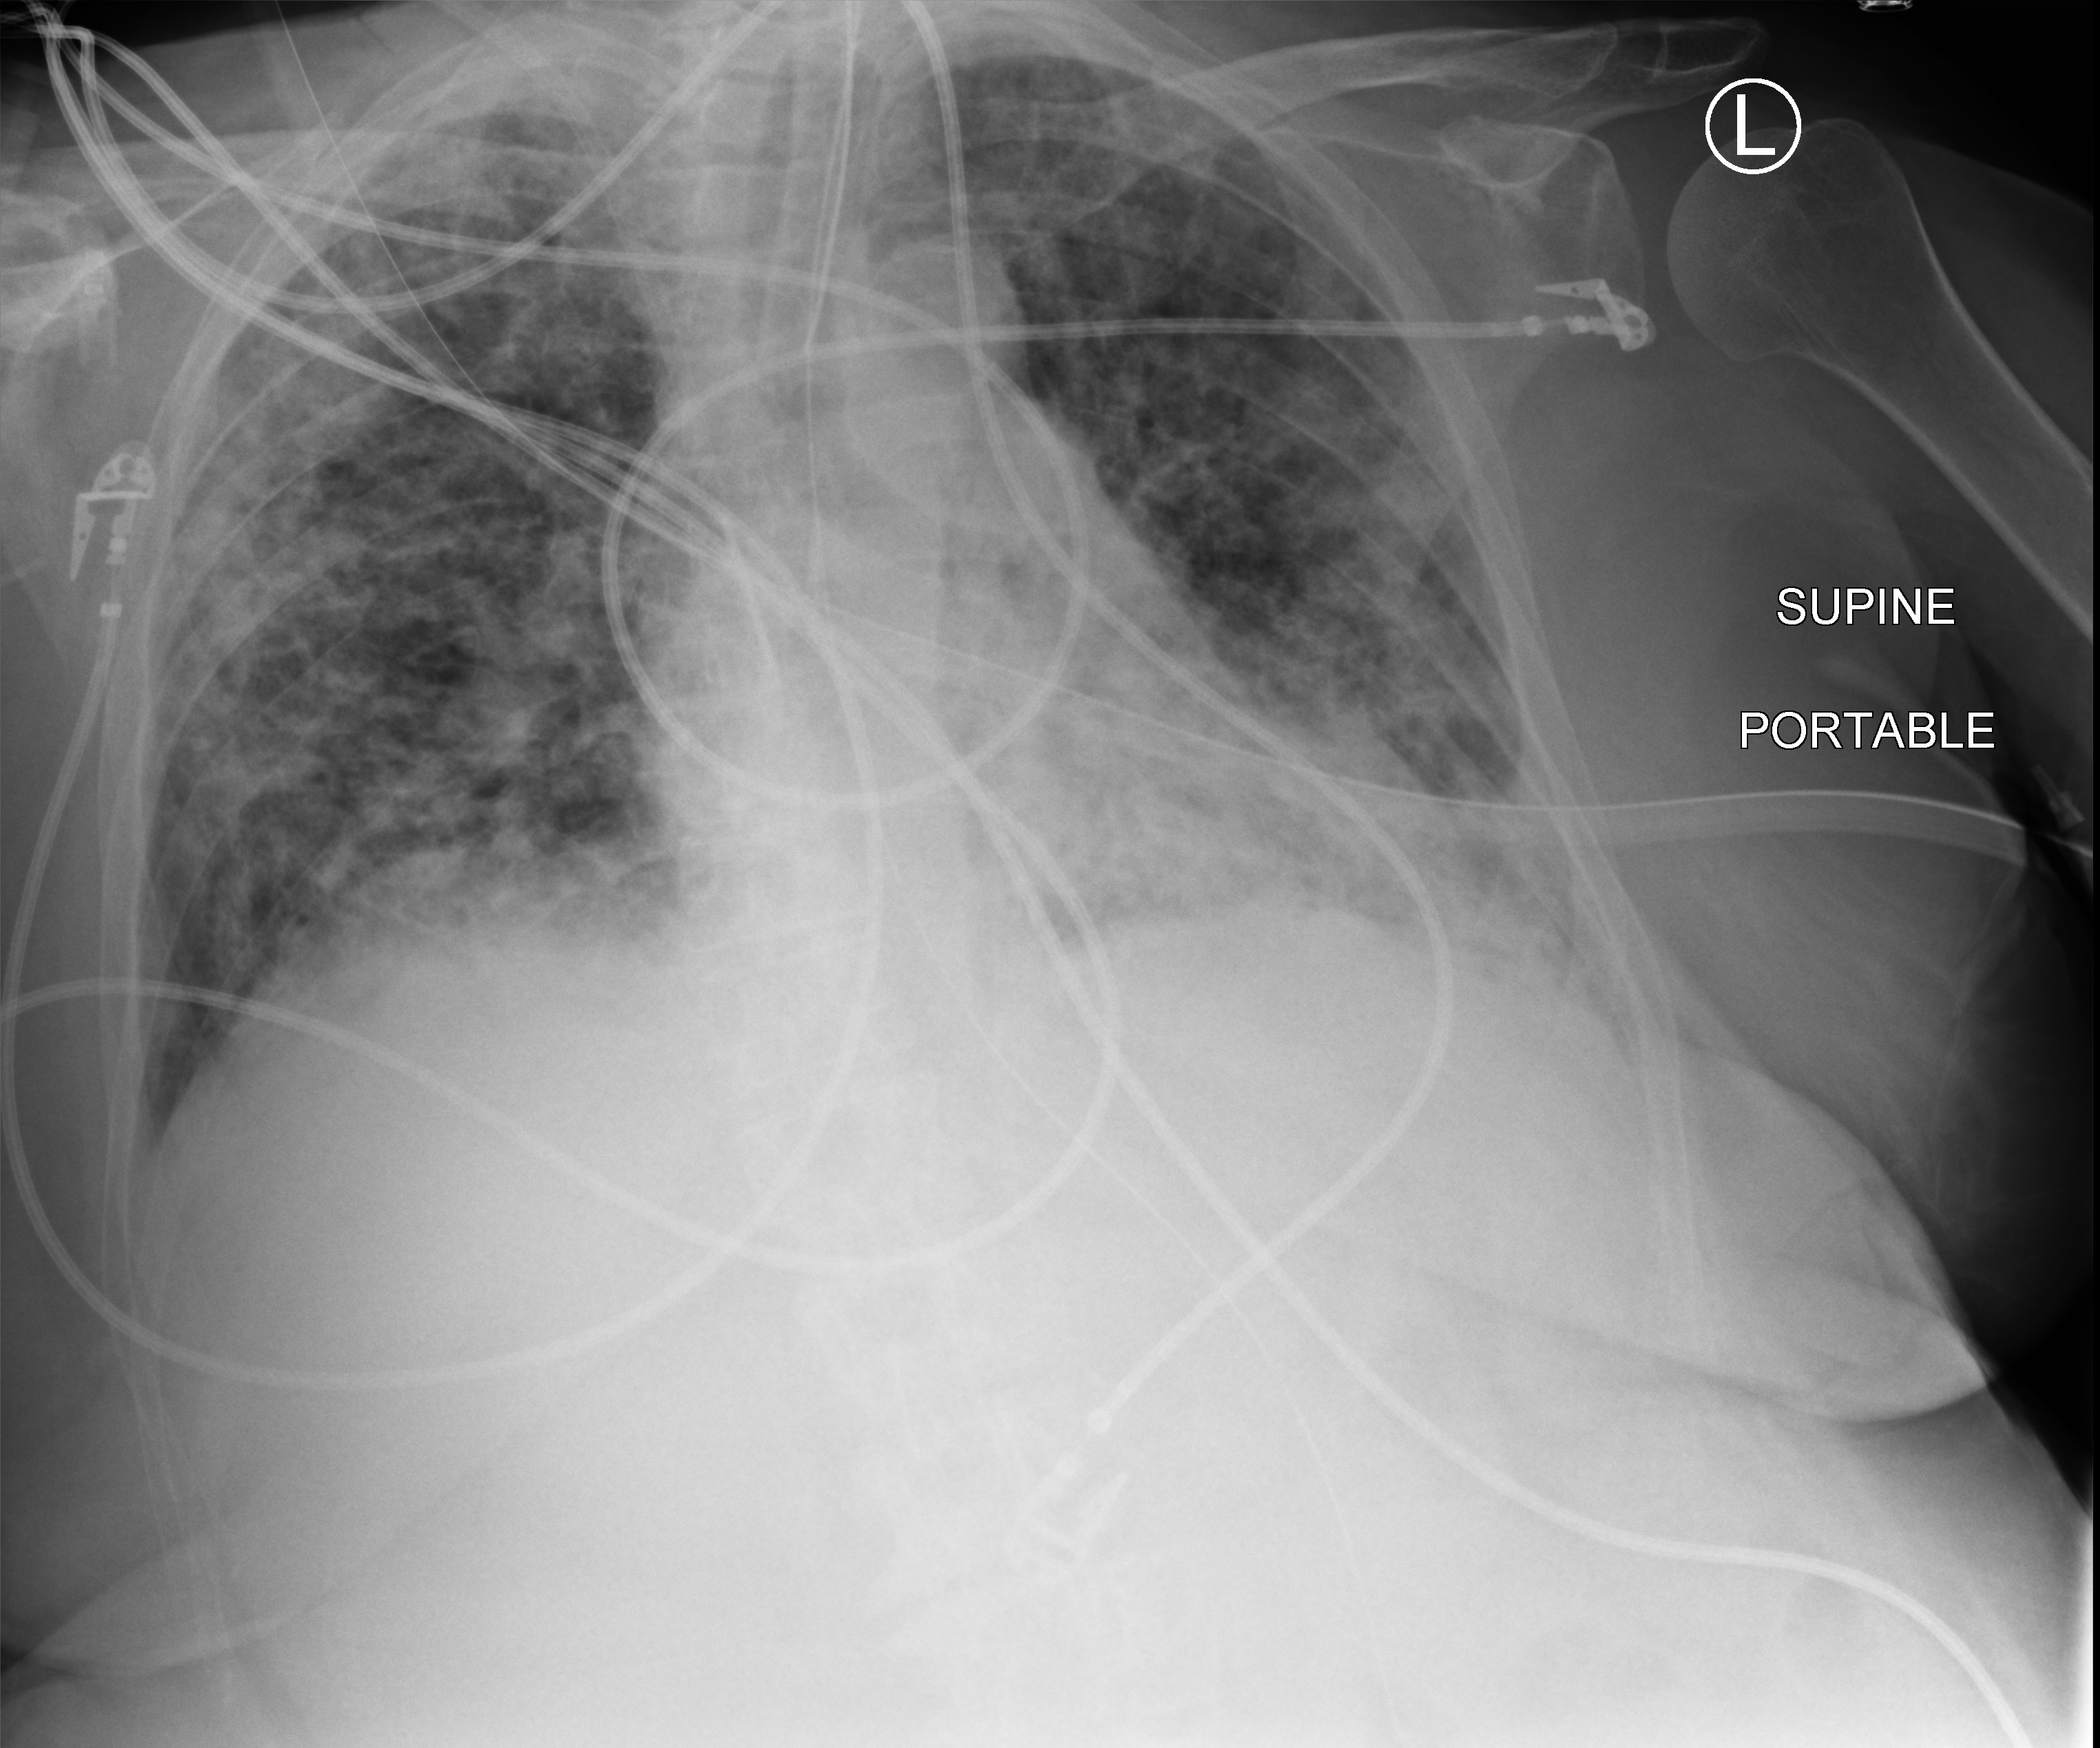
Bedside chest radiograph (computed radiography). Female patient hospitalised with COVID-19, age 75–90 years.
From the hospital-stay record, not from the radiograph (when in the stay this image was taken is not recorded): admitted to intensive care during this hospital stay: yes.